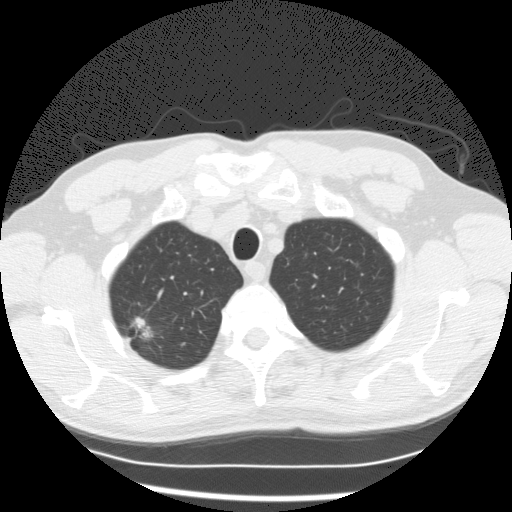
Chest CT (low-dose screening protocol), one axial image, first (baseline) screen, lung window (W 1500 / L -600 HU), 2.5 mm slice thickness, standard (soft-tissue) reconstruction kernel (STANDARD), slice 20 of 132 in the series. Male, age 63 years at enrolment. Current smoker at enrolment.
Expert reader's lesion annotation, bounding box [x1, y1, x2, y2] px = [107, 298, 175, 363]. Reader record for this screening exam (exam-level; its link to the box is not recorded): non-calcified nodule or mass ≥4 mm, right upper lobe, 19 × 9 mm, poorly defined margins, mixed attenuation. Official screen result: positive, change unspecified: nodule(s) >= 4 mm or enlarging nodule(s), mass(es), or other non-specific abnormalities suspicious for lung cancer. Later outcome: lung cancer diagnosed 152 days after this screen — bronchiolo-alveolar adenocarcinoma, NOS, right upper lobe, moderately differentiated (G2), stage IA (AJCC 6th edition), 15 mm at pathology.